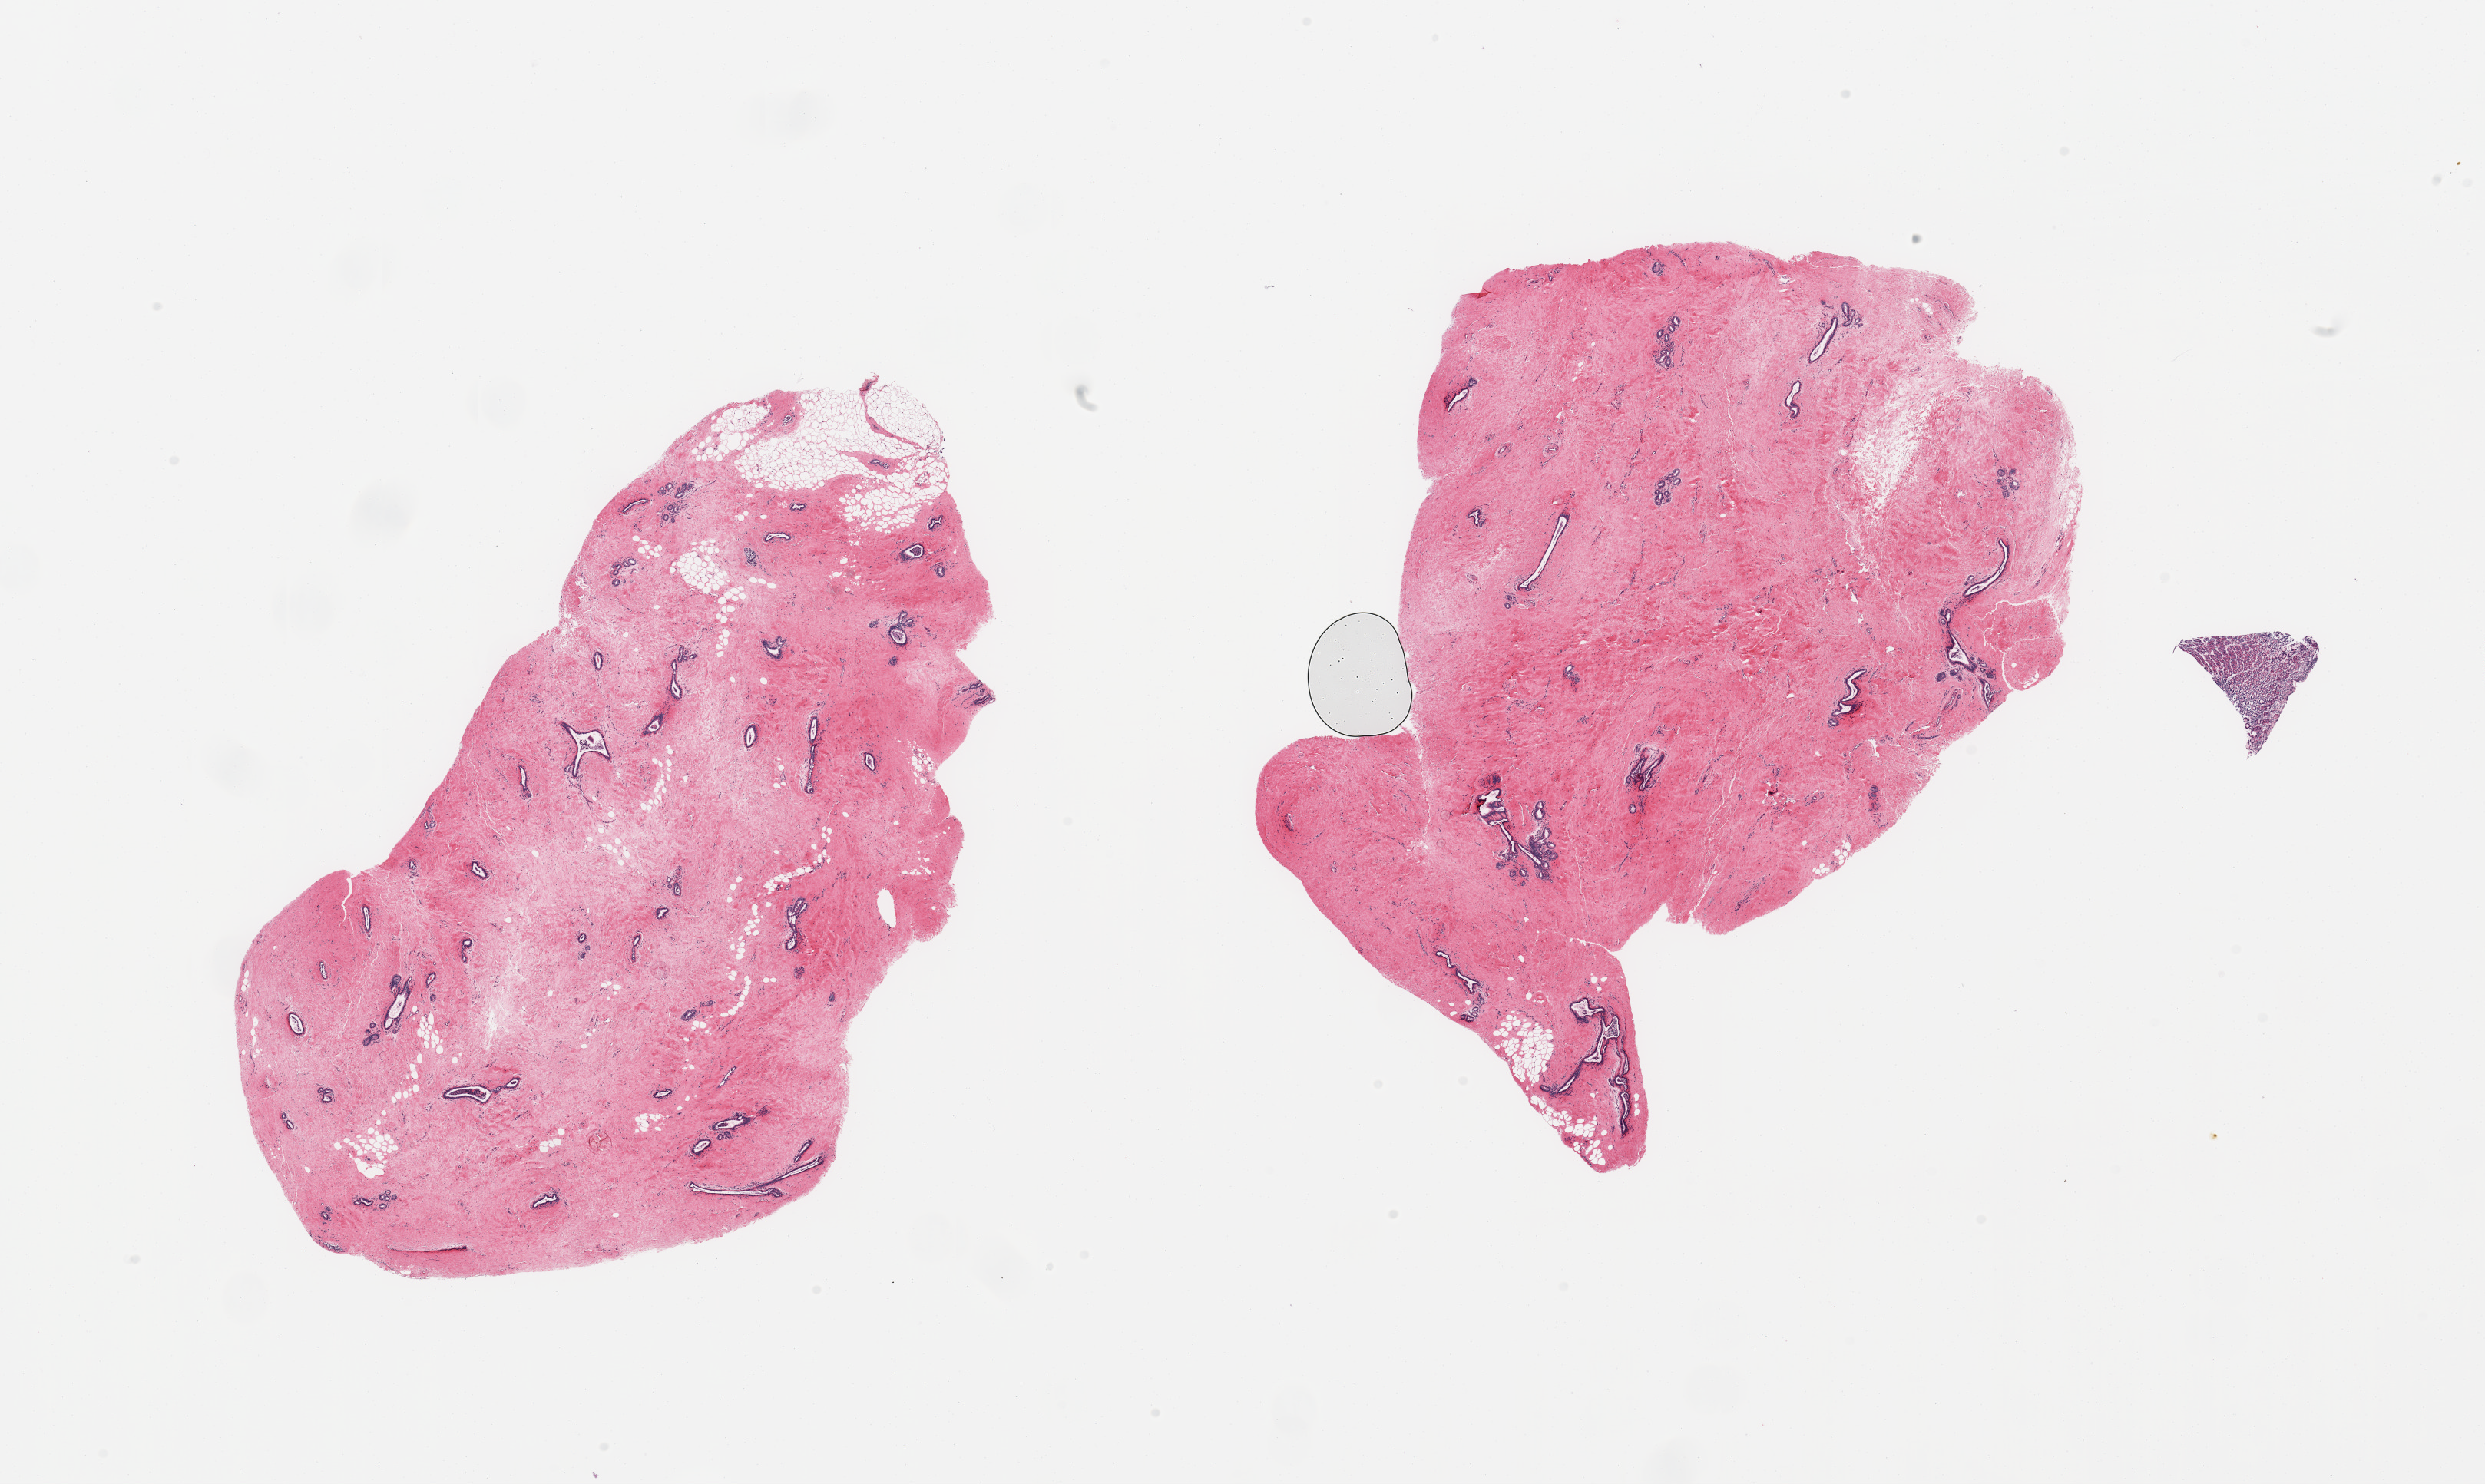
H&E whole-slide image, brightfield, shown as a low-resolution overview of the whole scanned area (about 25.6 x 15.3 mm, from a 20x scan); PAXgene-fixed paraffin-embedded (PFPE) section; target tissue: breast; tissue donor sample.
• review note (as recorded): 2 pieces; minimal fat, predominantly dense fibrocollagenous stroma with numerous embedded ducts; detached floater